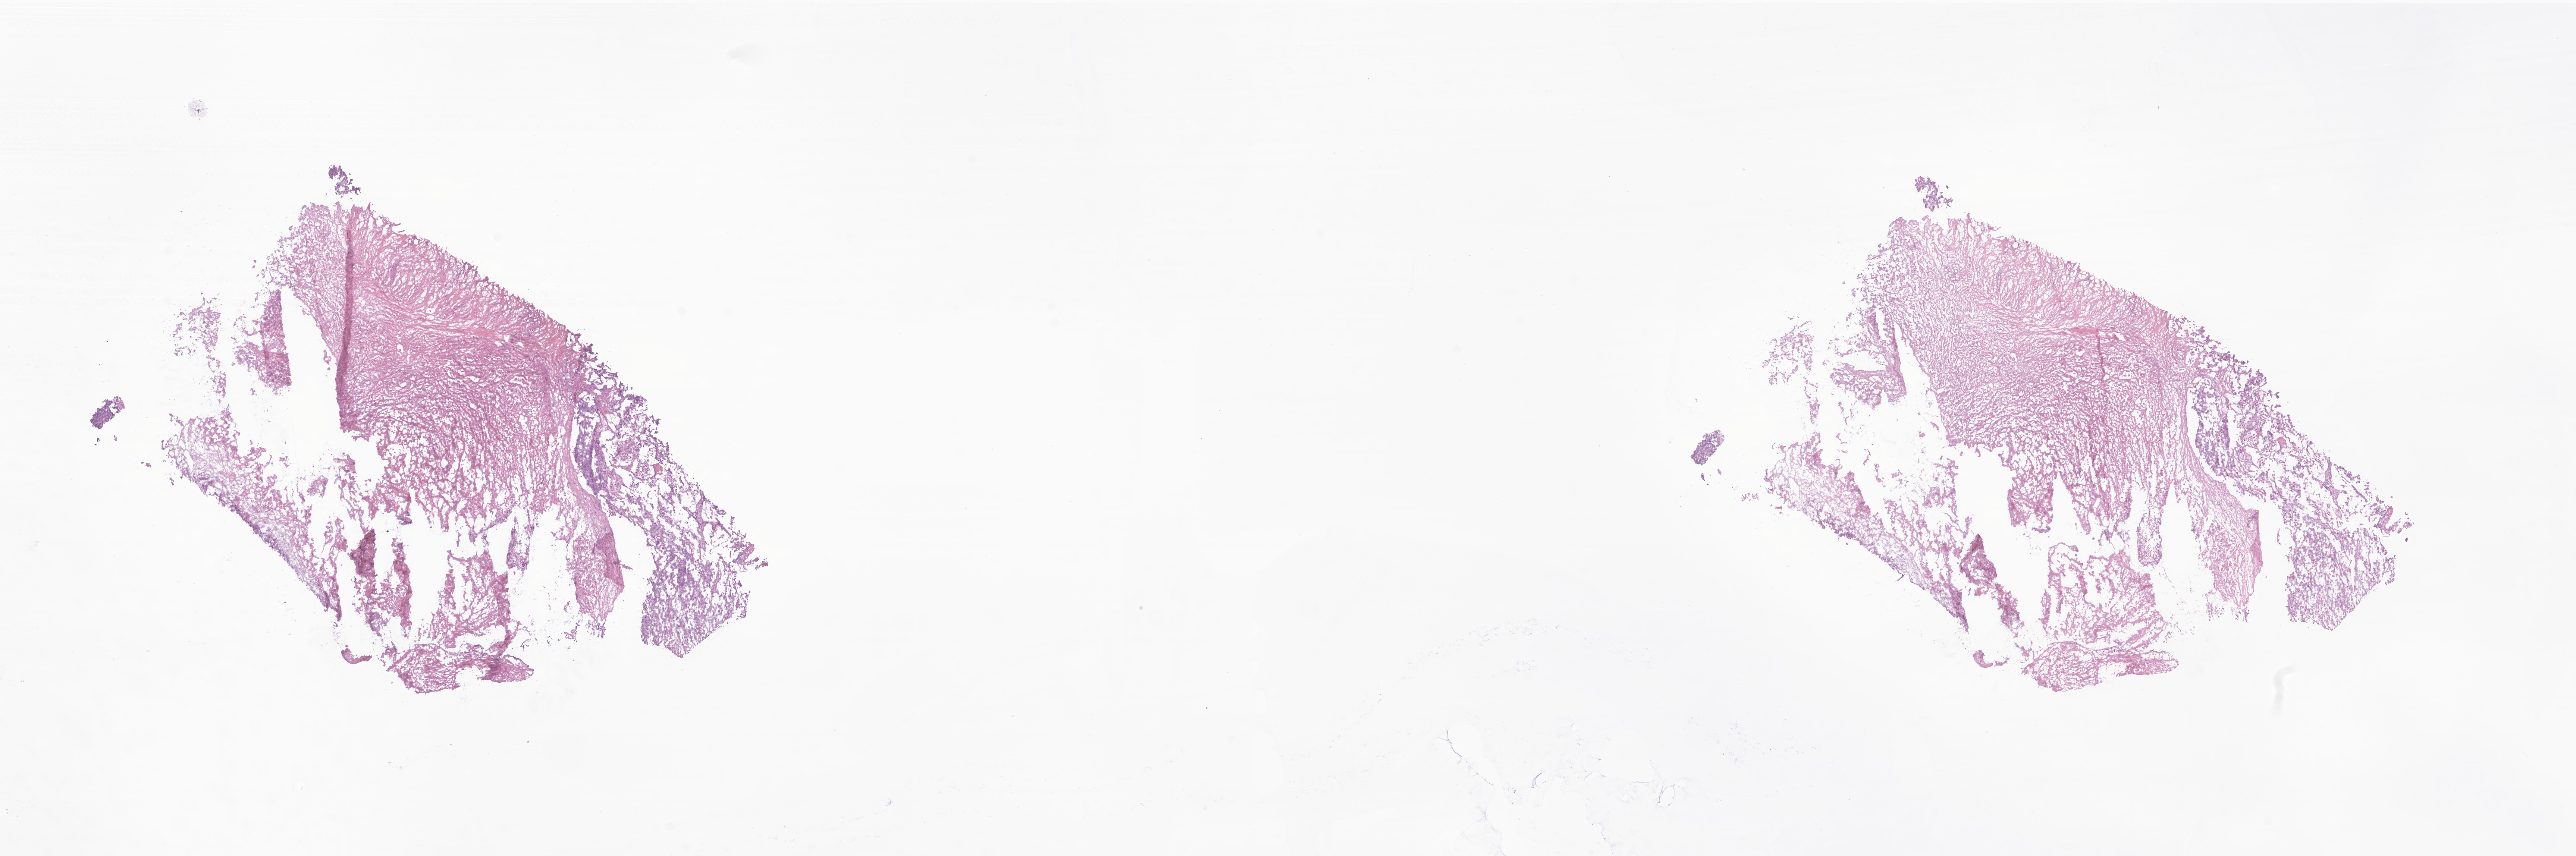
Hematoxylin and eosin (H&E) whole-slide image of tumor tissue from the brain — a low-resolution overview of the entire scanned area, about 29.1 x 9.7 mm; cryosection (OCT / tissue freezing medium). Patient male; age 47 months (3 years 11 months).
Diagnosis: Neoplasm, uncertain whether benign or malignant.